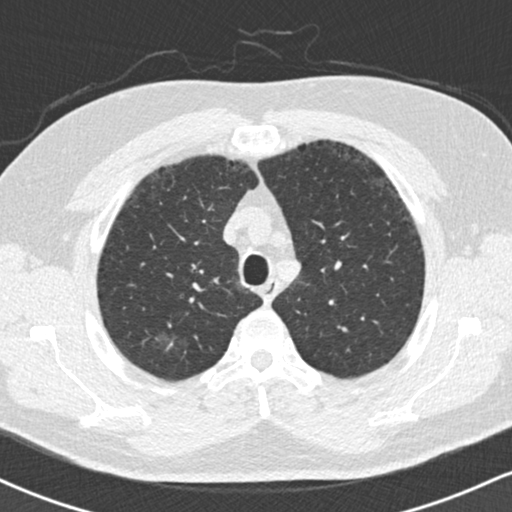
Chest CT (low-dose screening protocol), one axial image; second annual screen; lung window (W 1500 / L -600 HU); 120 kVp; 512 × 512 image matrix. Male participant, aged 59 years at enrolment. Current smoker at enrolment.
• Expert reader's lesion annotation, bounding box <151,314,202,366> (left, top, right, bottom; pixels).
• Screening reader's record for this exam (one nodule recorded; not confirmed to be the boxed lesion): non-calcified nodule or mass ≥4 mm, right upper lobe, 18 × 16 mm, ground glass attenuation, pre-existing on the prior screen: yes.
• Participant outcome: lung cancer diagnosed 60 days after this screen — bronchiolo-alveolar adenocarcinoma, NOS, right lower lobe, stage IA (AJCC 6th edition), 15 mm at pathology.